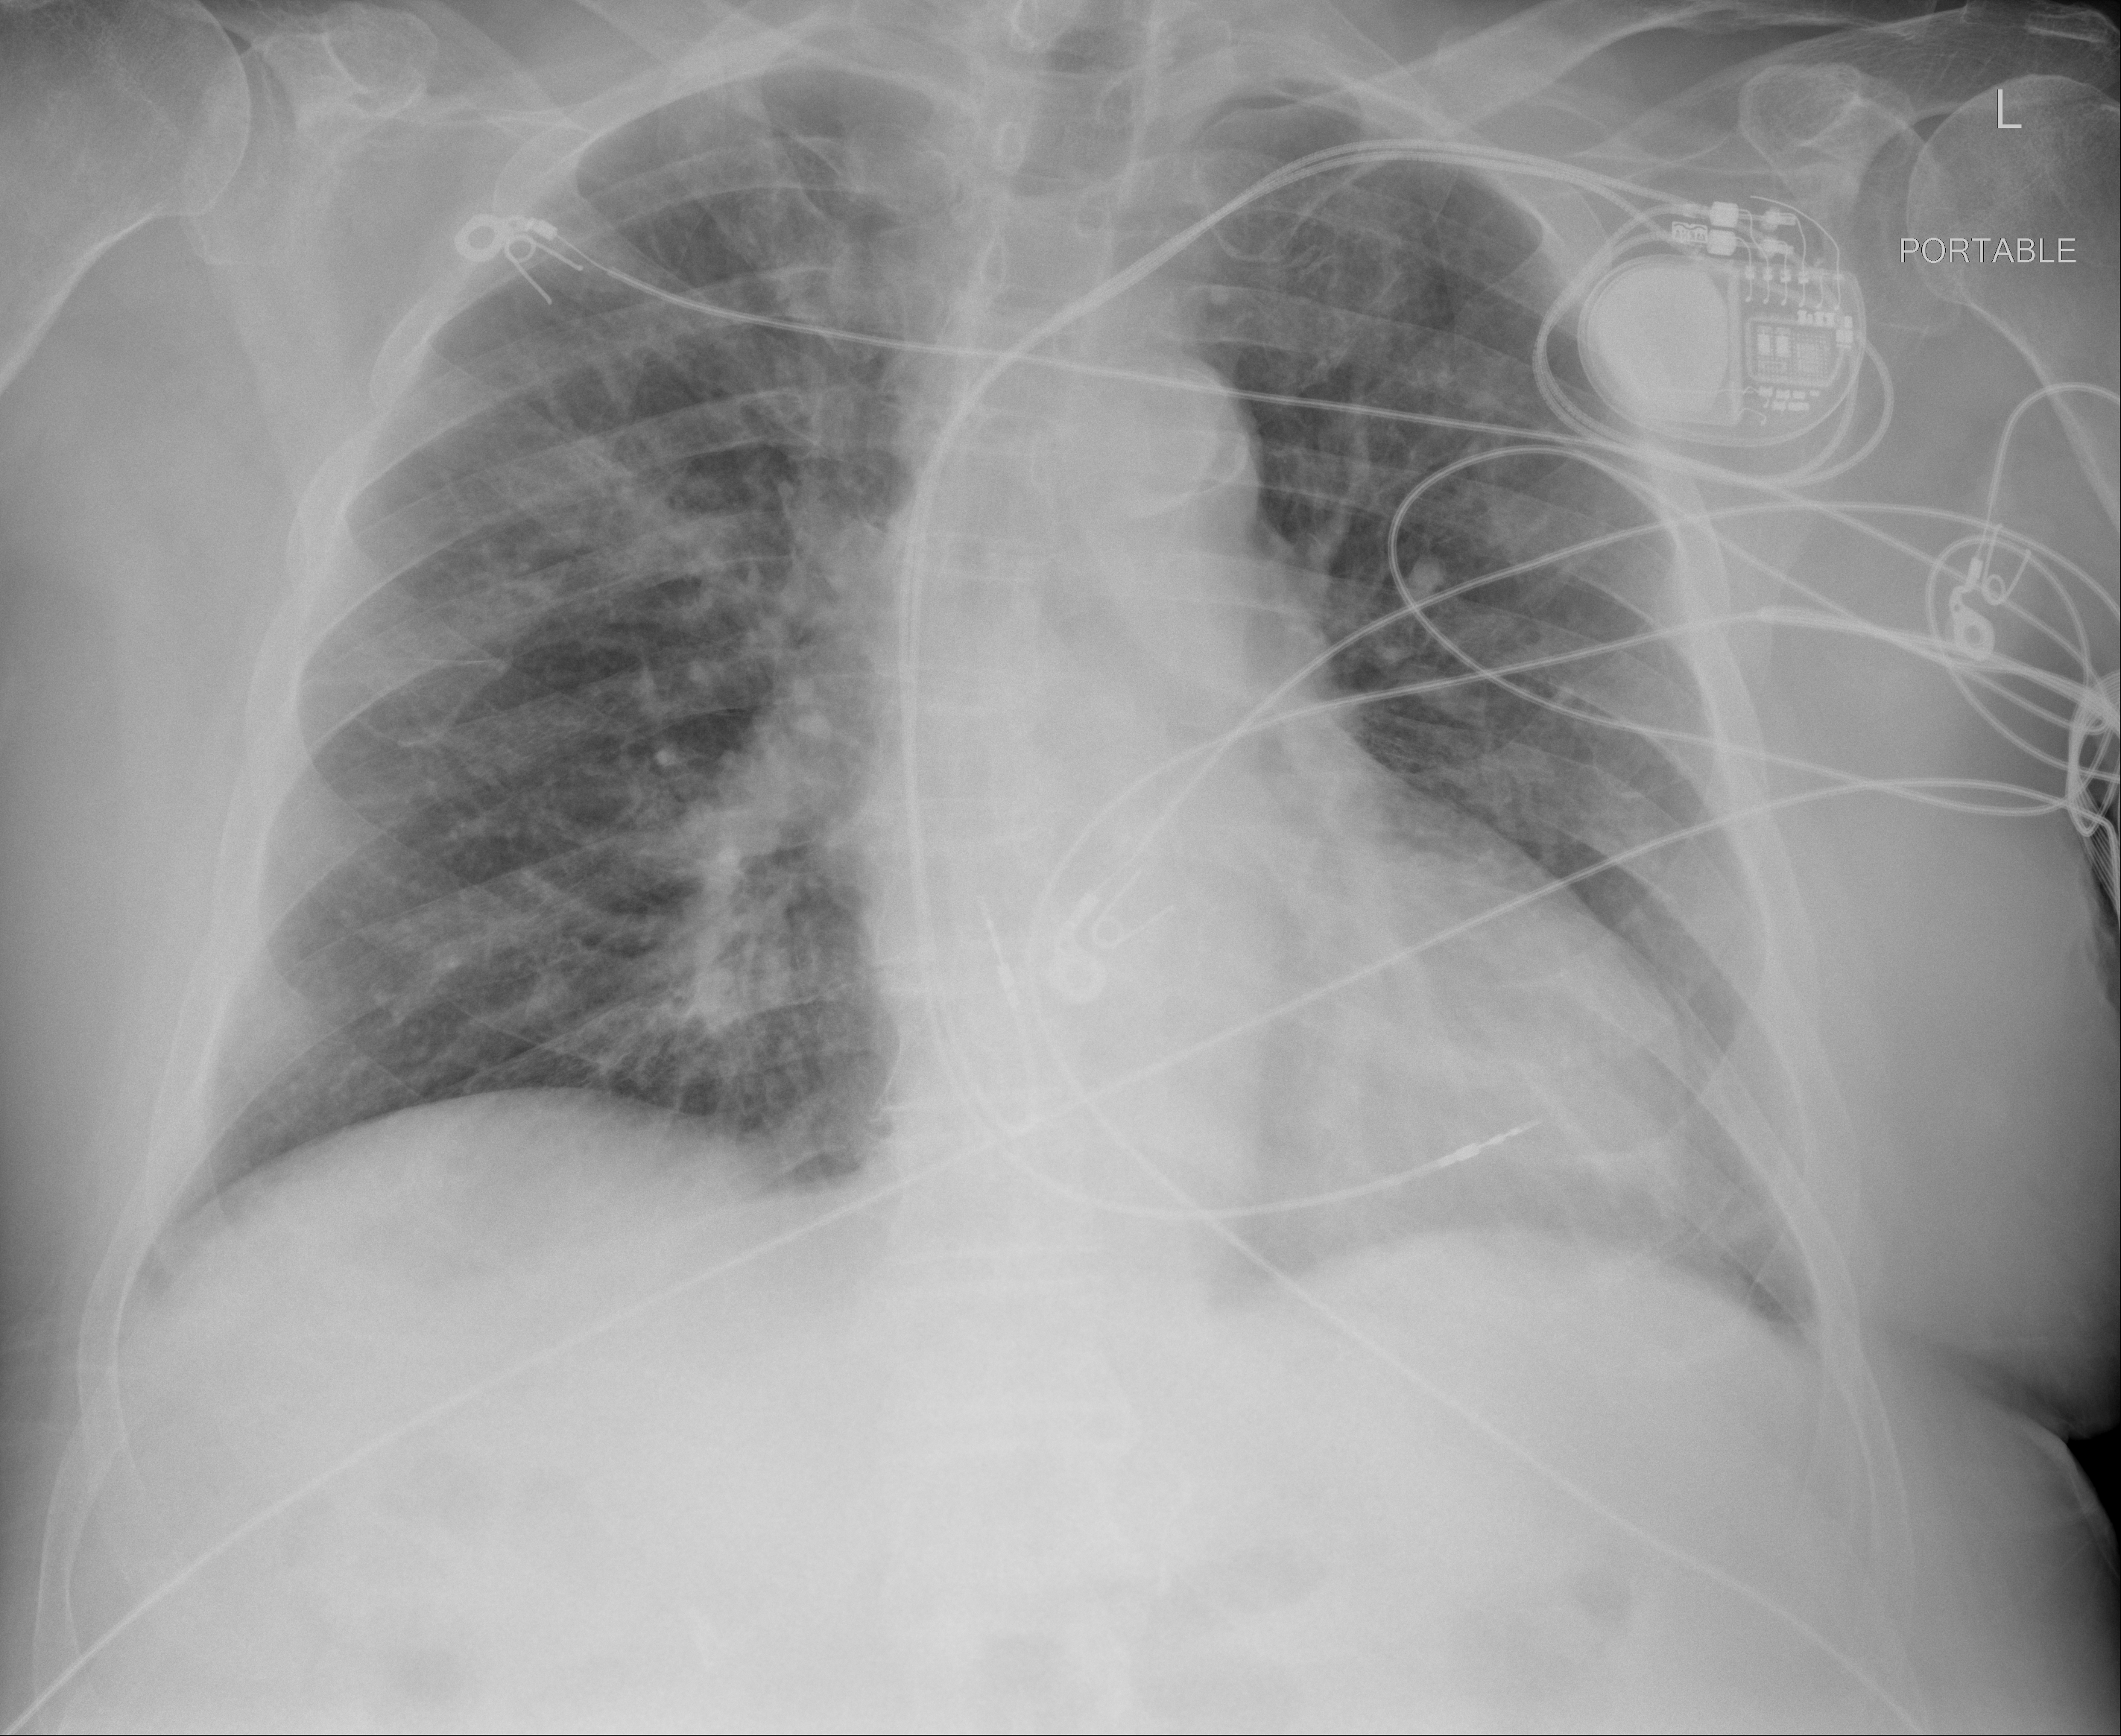
Chest radiograph, AP projection. Male patient, age 88 years; imaged 2 days after the COVID-19 diagnosis.
Radiologist key findings (as recorded): There is also interval improvement in the left retrocardiac airspace disease with the peribronchovascular changes noted. There is interval development of minimal peribronchovascular airspace disease in the right upper lobe.